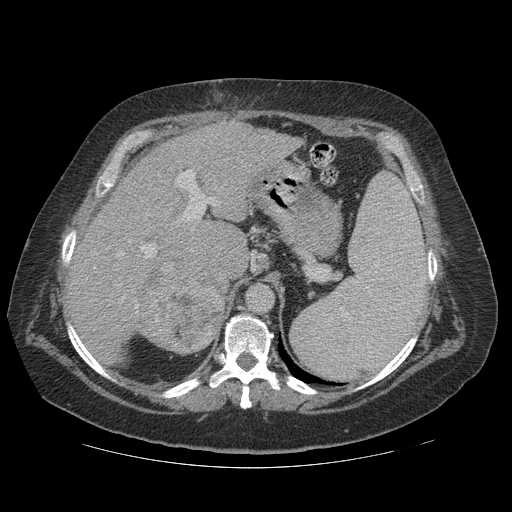
Contrast-enhanced abdominal CT (liver protocol), one axial slice; position 81 of 121 along the scan axis; soft-tissue window (W 400 / L 40 HU); 2.5 mm slice thickness; 512 × 512 image matrix, field of view 420 × 420 mm. Case-level facts recorded for this patient, not image findings: diagnosis: hepatocellular carcinoma (patient treated with transarterial chemoembolisation; whether this scan precedes or follows treatment is not stated here); TNM stage (as recorded): Stage-IIIA; Child-Pugh class: A; tumour differentiation: well differentiated; tumour nodularity: multinodular.
Annotated regions visible in this slice (semi-automatically segmented with operator editing):
- liver parenchyma outside the tumour (the mass and vessels are separate outlines, so this box may not span the whole liver): bounding box (x1, y1, x2, y2) in pixels: (66, 120, 303, 360)
- mass: (134, 249, 227, 354)
- liver vessels: (75, 170, 221, 320)